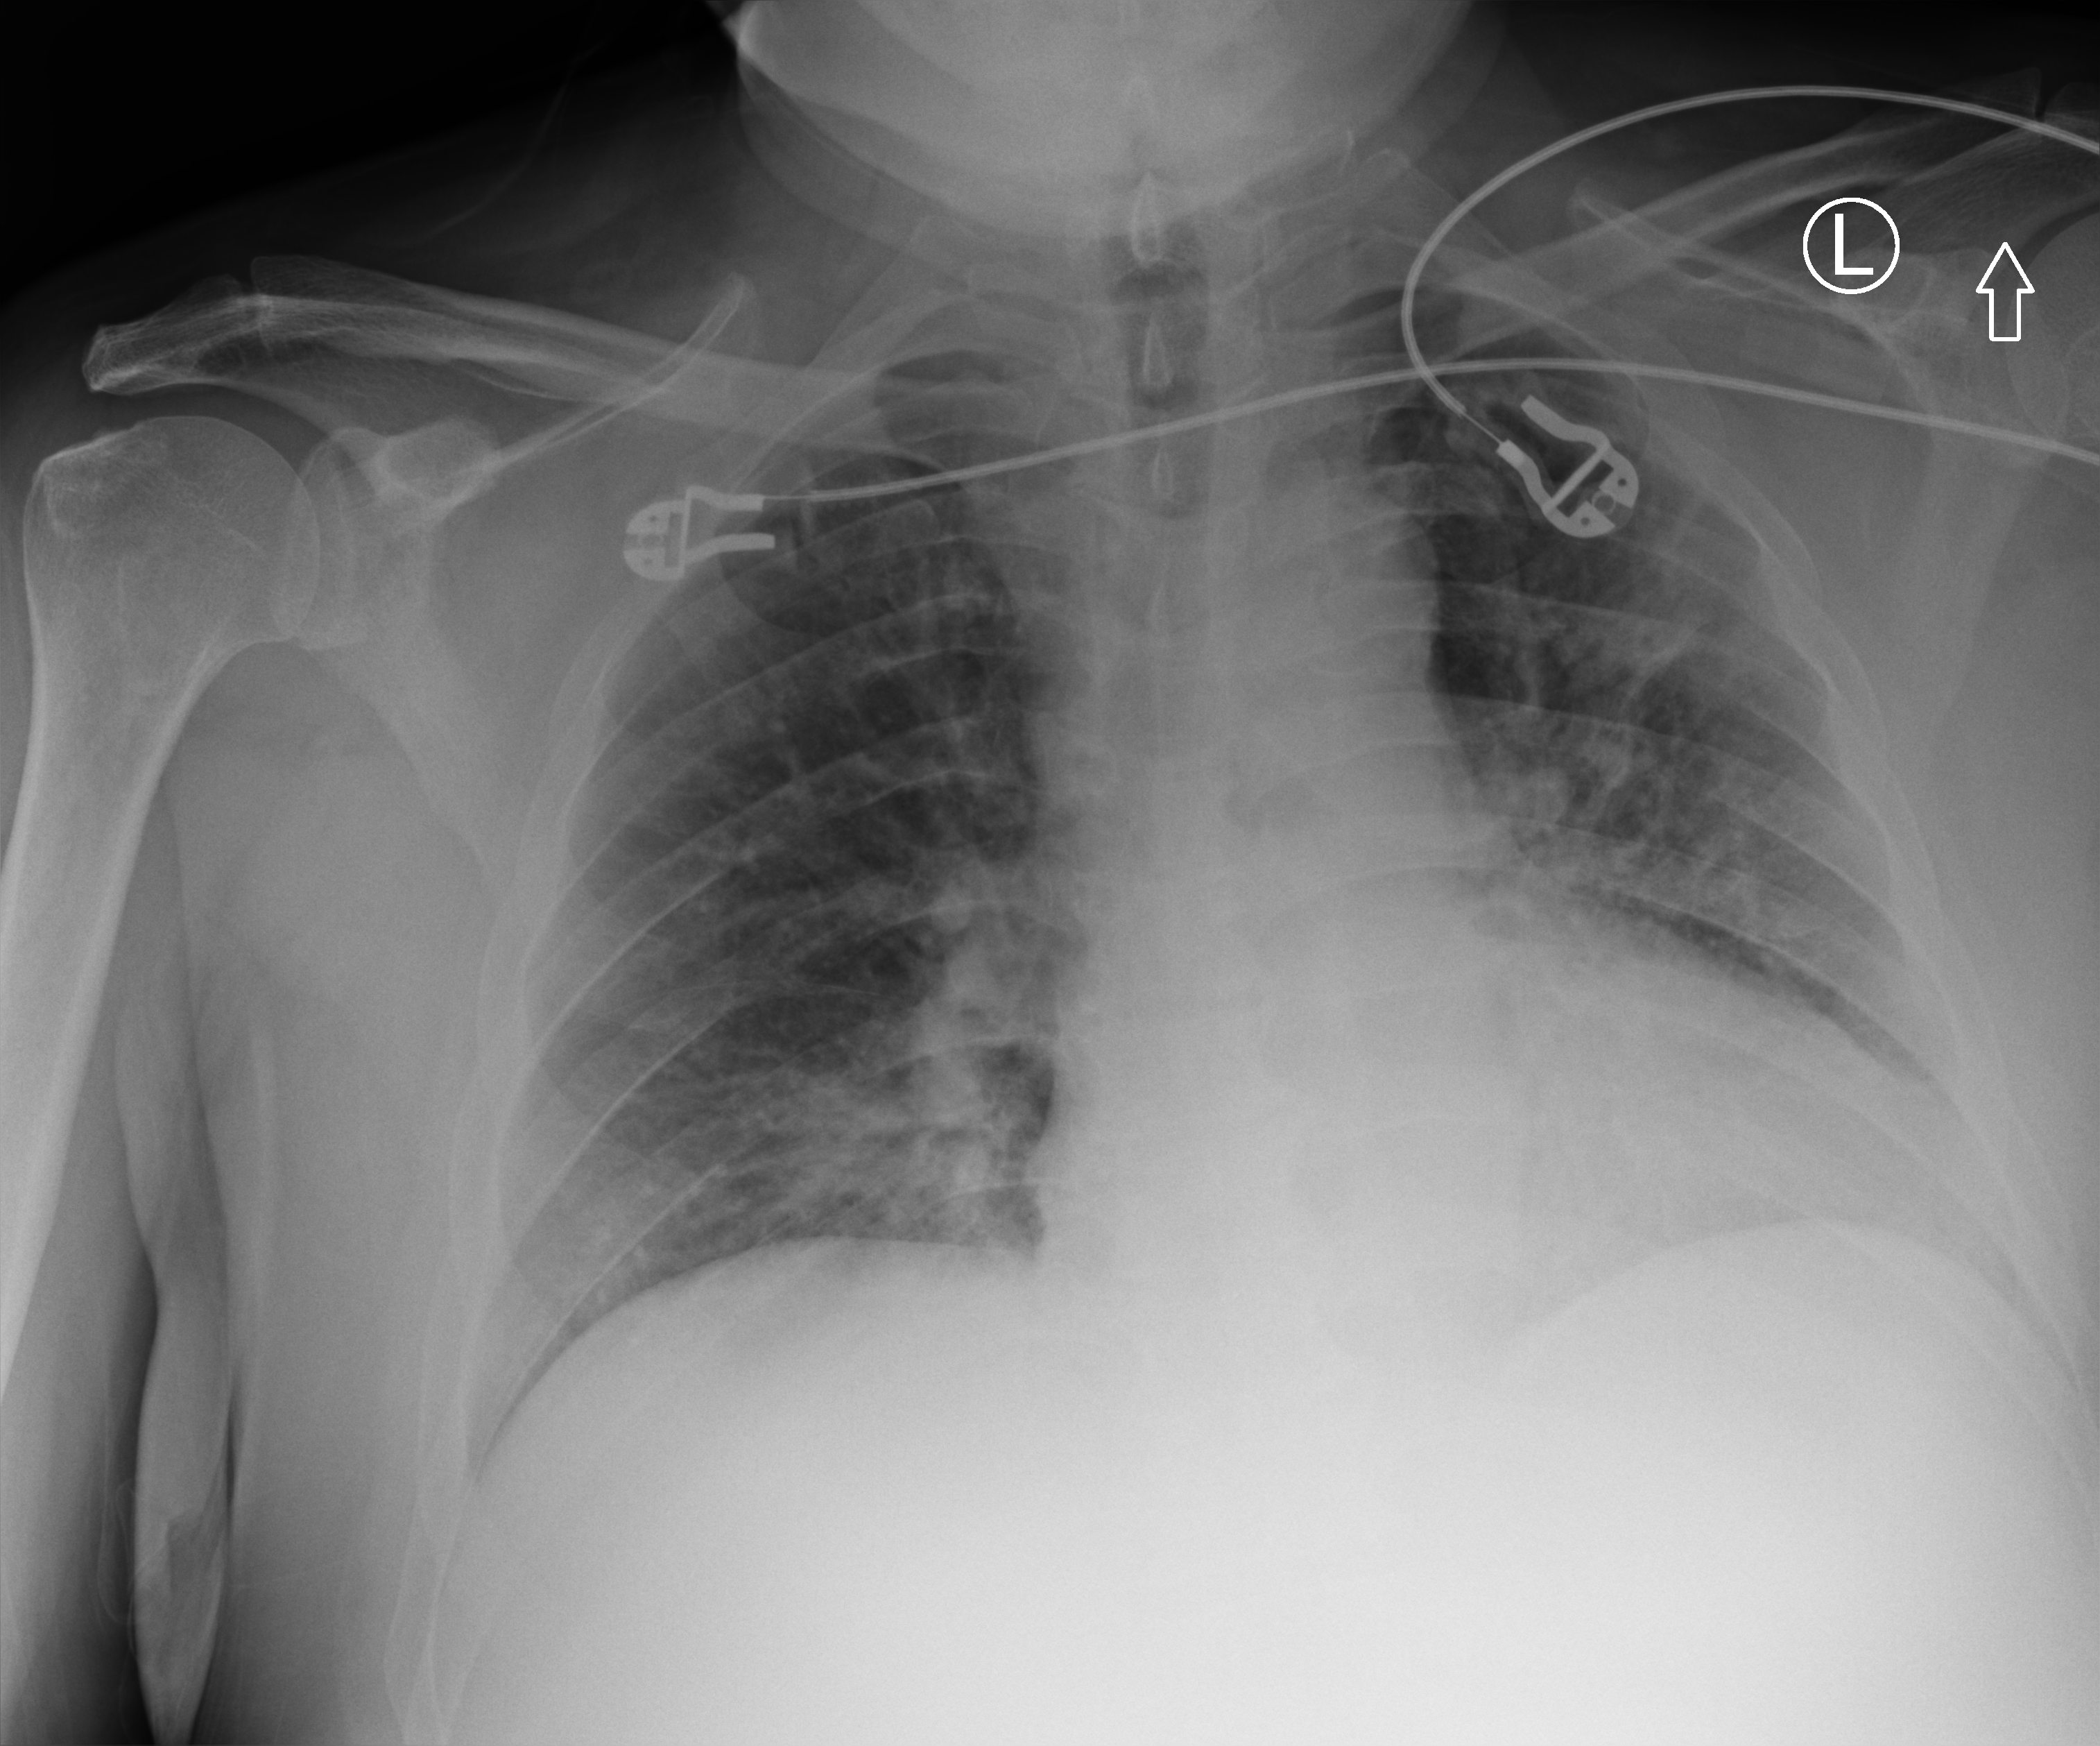
Portable chest radiograph; anteroposterior (AP) projection. Male patient hospitalised with COVID-19, age 18–59 years.
Admission-level facts for this patient (not findings on this image; timing relative to this image not recorded): smoking status (admission record): former; admitted to intensive care during this hospital stay: no.